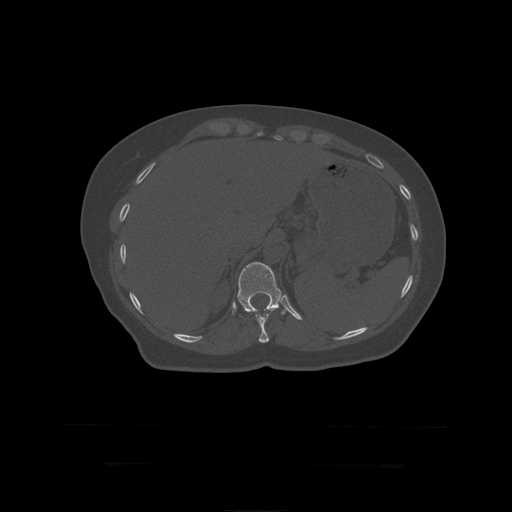
CT including the spine, one axial slice. Position 207 of 399 along the scan axis. Reconstruction kernel STANDARD. Bone window (W 1800 / L 400 HU). 1.25 mm slice thickness. 512 × 512 image matrix, field of view 450 × 450 mm. Patient age 41 years. Case-level facts recorded for this patient, not image findings: primary cancer: breast.
Structures marked on this image (semi-automatic segmentation, software-assisted and operator-edited):
- T11 vertebra: bounding box (x1, y1, x2, y2) in pixels: (248, 309, 274, 343)
- T12 vertebra: (237, 262, 291, 315)